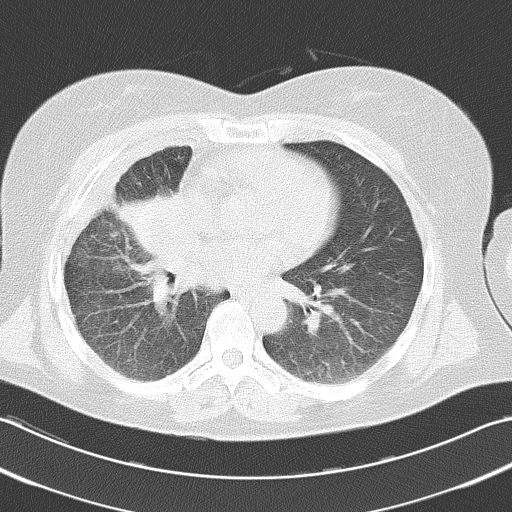
Chest CT, one axial slice; slice 15 of 38 in the series (ordered by position); reconstruction kernel B70f; lung window (W 1500 / L -600 HU); 512 × 512 image matrix, field of view 346 × 346 mm. Female patient, age 52 years. Case-level facts recorded for this patient, not image findings: clinical TNM (as recorded): T3 N1 M0.
Outlined on this slice (bounding box drawn by a radiologist):
- lung tumour (recorded histology: squamous cell carcinoma): bounding box <114,185,192,303> (left, top, right, bottom; pixels)